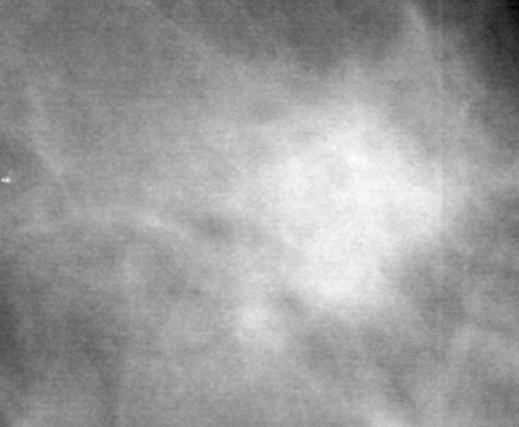
Crop from a digitized film mammogram around one marked abnormality, right breast, MLO view, BI-RADS breast density category 3 (scale 1–4).
Finding: mass, shape irregular, margins ill defined; BI-RADS assessment category 4; pathology (as recorded): benign.